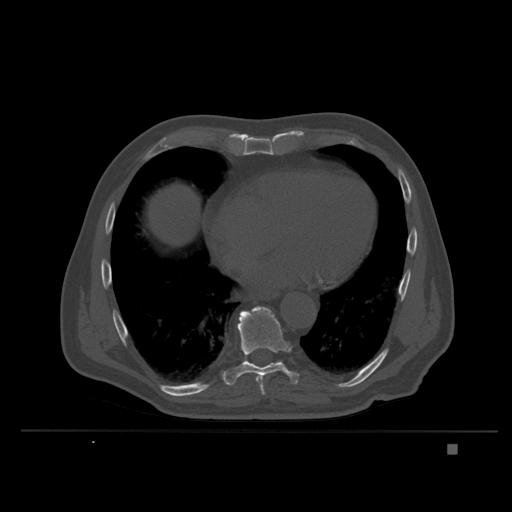
CT including the spine, one axial slice; slice 212 of 435 in the series (ordered by position); bone window (W 1800 / L 400 HU); 1.5 mm slice thickness; 512 × 512 image matrix, field of view 434 × 434 mm. Patient: male, 73 years. From the clinical record (not read from this slice): primary cancer: skin.
Structures marked on this image (semi-automatic segmentation, software-assisted and operator-edited):
- T9 vertebra: bounding box <223,306,299,395> (left, top, right, bottom; pixels)